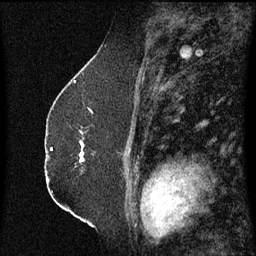
Breast MRI (dynamic contrast-enhanced), one sagittal slice. Dynamic contrast-enhanced series, image 2 of 3 at this slice position (ordered by acquisition). 1.5 T. TE 4.2 ms, TR 8.4 ms. 2.3 mm slice thickness. 256 × 256 image matrix, field of view 200 × 200 mm. Patient: female, 52 years. From the clinical record (not read from this slice): setting: breast cancer imaged before/during neoadjuvant chemotherapy; receptor status: HR-positive, HER2-negative.
Structures marked on this image (semi-automatically segmented with operator editing):
- analysis volume of interest (the breast-tissue region the enhancement analysis was run in; not a lesion): bounding box [x1, y1, x2, y2] px = [80, 132, 88, 165]
- tumour enhancement mask (voxels above the 70 % enhancement threshold inside the analysis volume of interest): [80, 142, 85, 163]